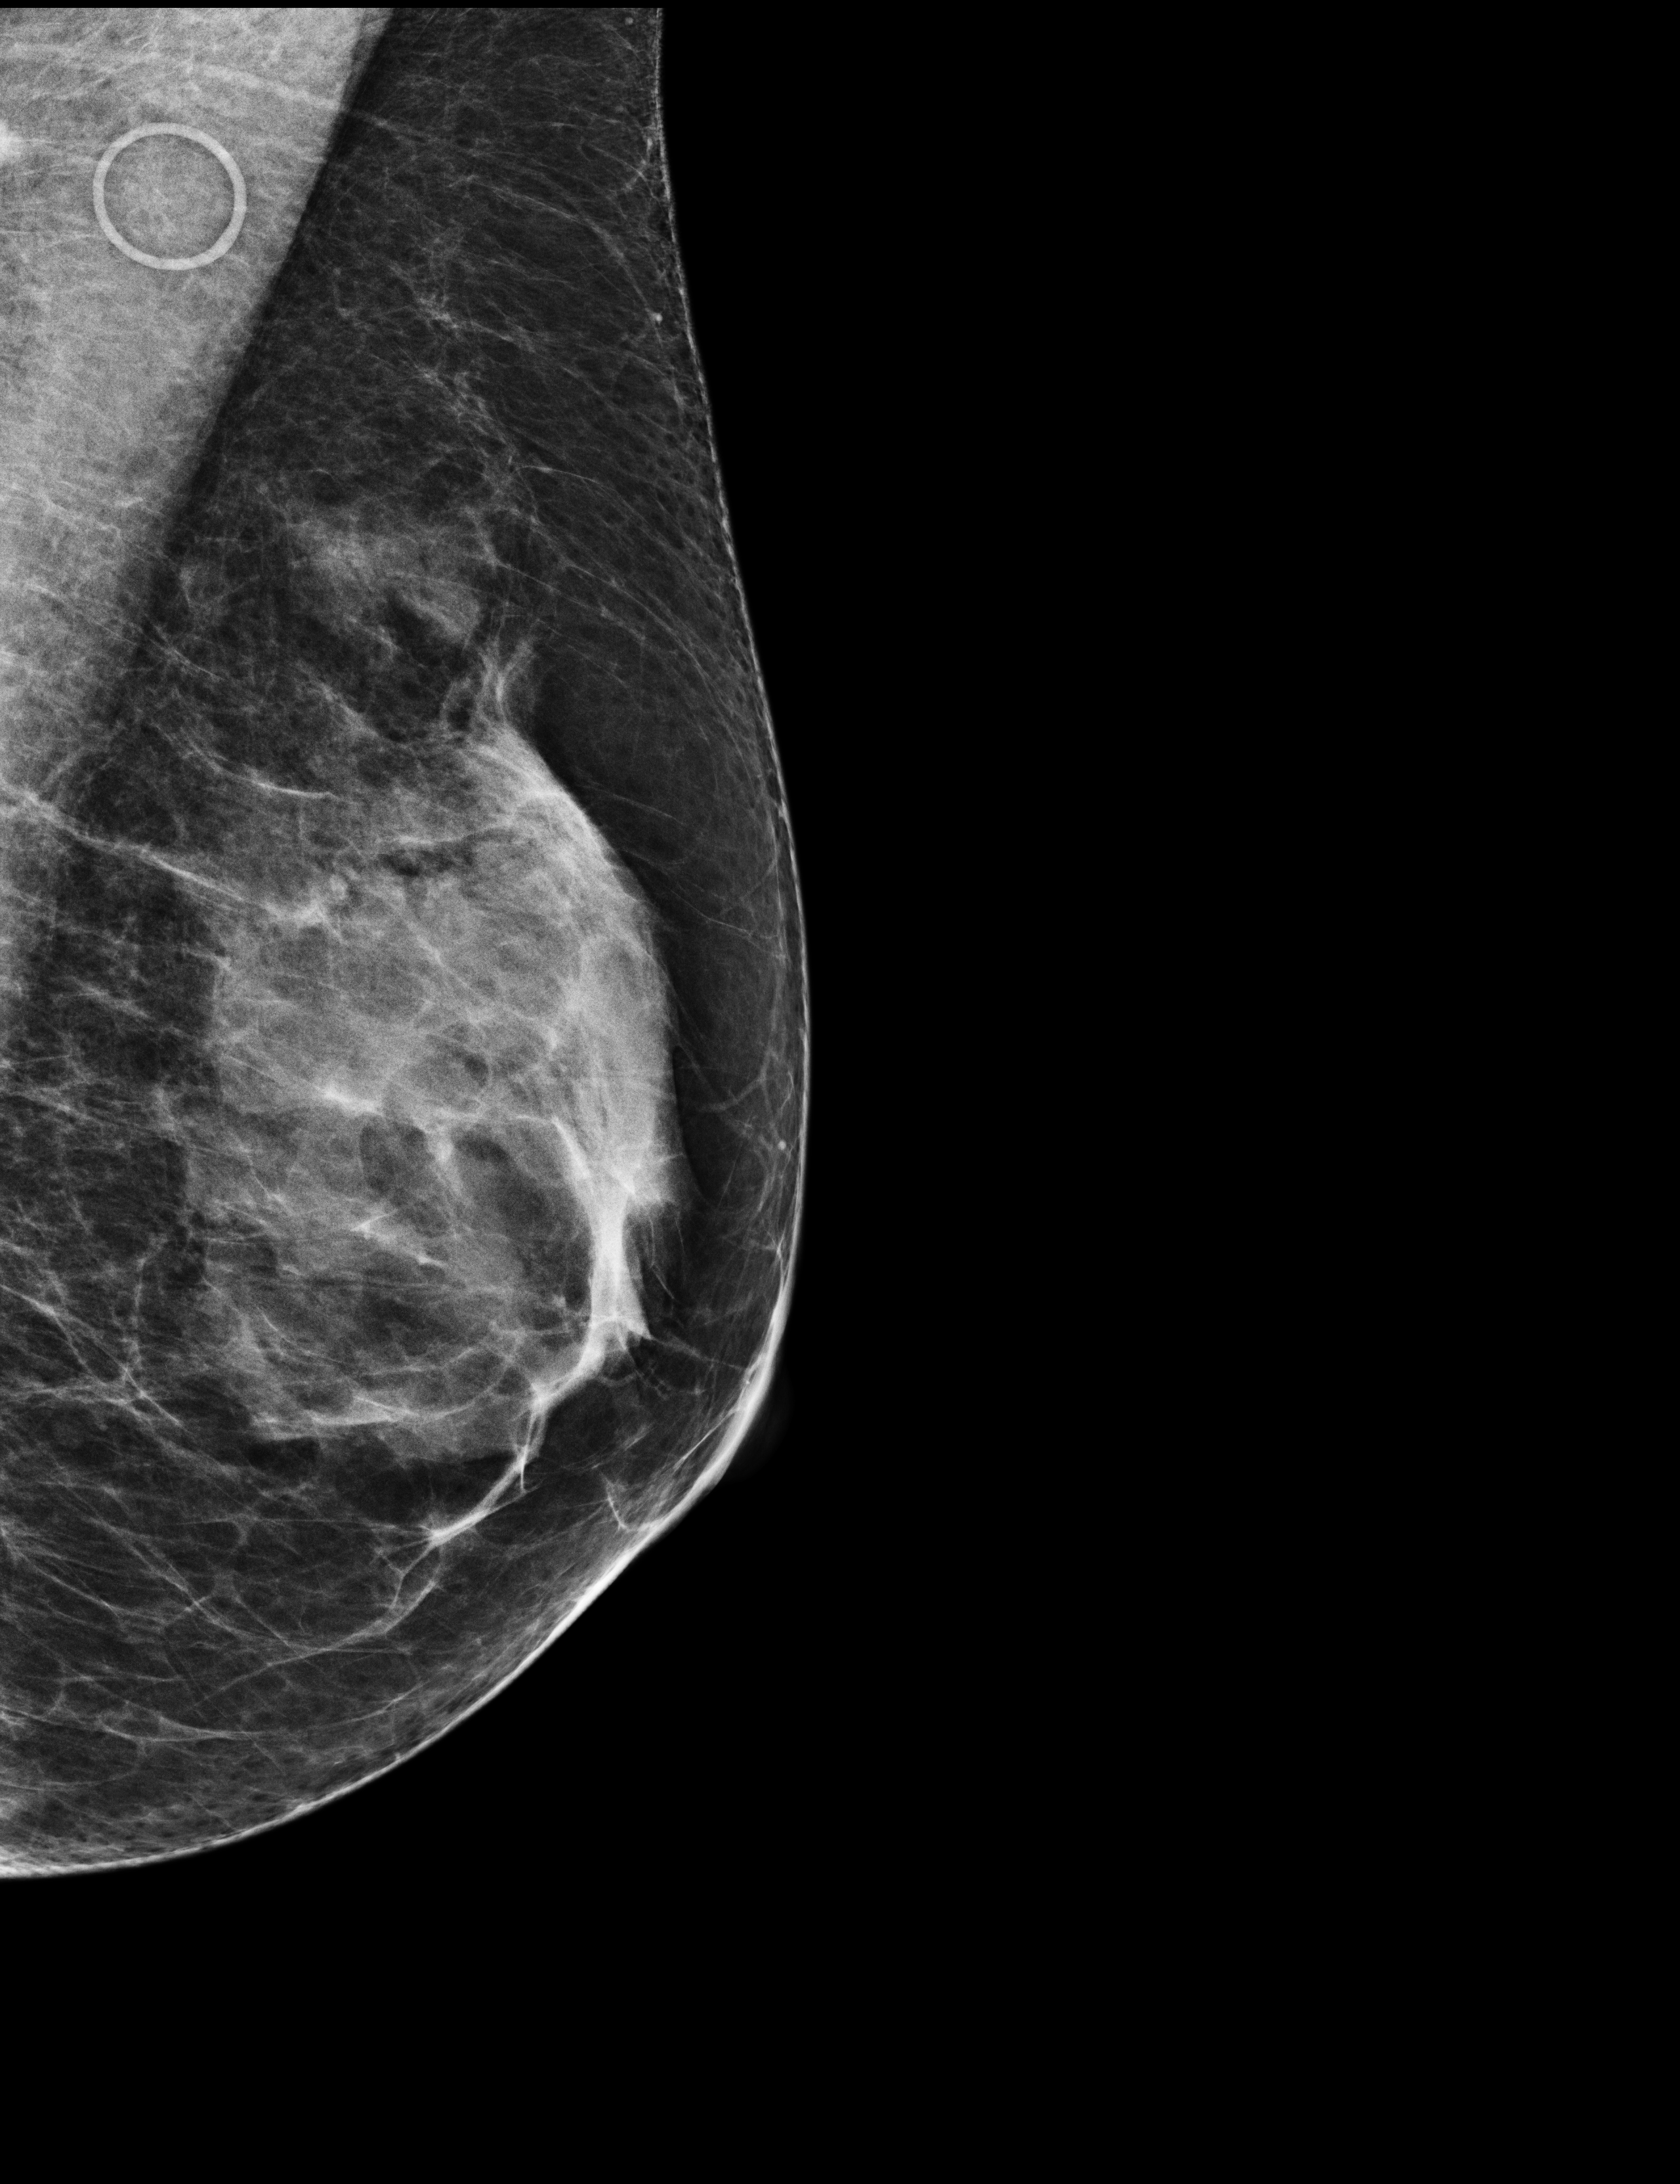
Digital mammogram (FFDM), left breast, MLO view, annual screening mammography examination, compressed breast thickness 55 mm. Patient: female, 66 years.
Breast density at the screening exam (both breasts): heterogeneously dense (BI-RADS density category c). Final BI-RADS assessment for this screening round (tomosynthesis exam, both breasts): category 1. Recall: no recall after this screen.